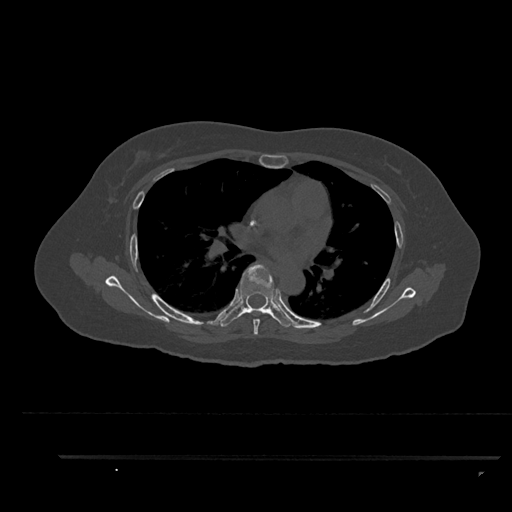
CT including the spine, one axial slice. Slice 573 of 797 in the series (ordered by position). Reconstruction kernel Br40s/3. Bone window (W 1800 / L 400 HU). 0.5 mm slice thickness. 512 × 512 image matrix, field of view 408 × 408 mm. Patient: female, 44 years. From the clinical record (not read from this slice): primary cancer: renal; vertebrae with lytic lesions (as recorded): L1.
Annotated regions visible in this slice (semi-automatic segmentation, software-assisted and operator-edited):
- T5 vertebra: box from (x=253, y=319) to (x=260, y=335) px
- T6 vertebra: (x=220, y=262)–(x=295, y=328)